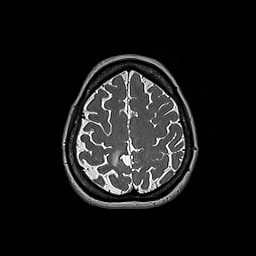
Brain MRI from a brain-tumour surgery series, one axial slice. 1 mm slice thickness. 256 × 256 image matrix, field of view 250 × 250 mm. From the clinical record (not read from this slice): histopathology: Oligodendroglioma; WHO grade: 2; IDH mutation: yes.
Outlined on this slice (manually delineated by an expert):
- tumour: bounding box (x1, y1, x2, y2) in pixels: (111, 150, 122, 170)